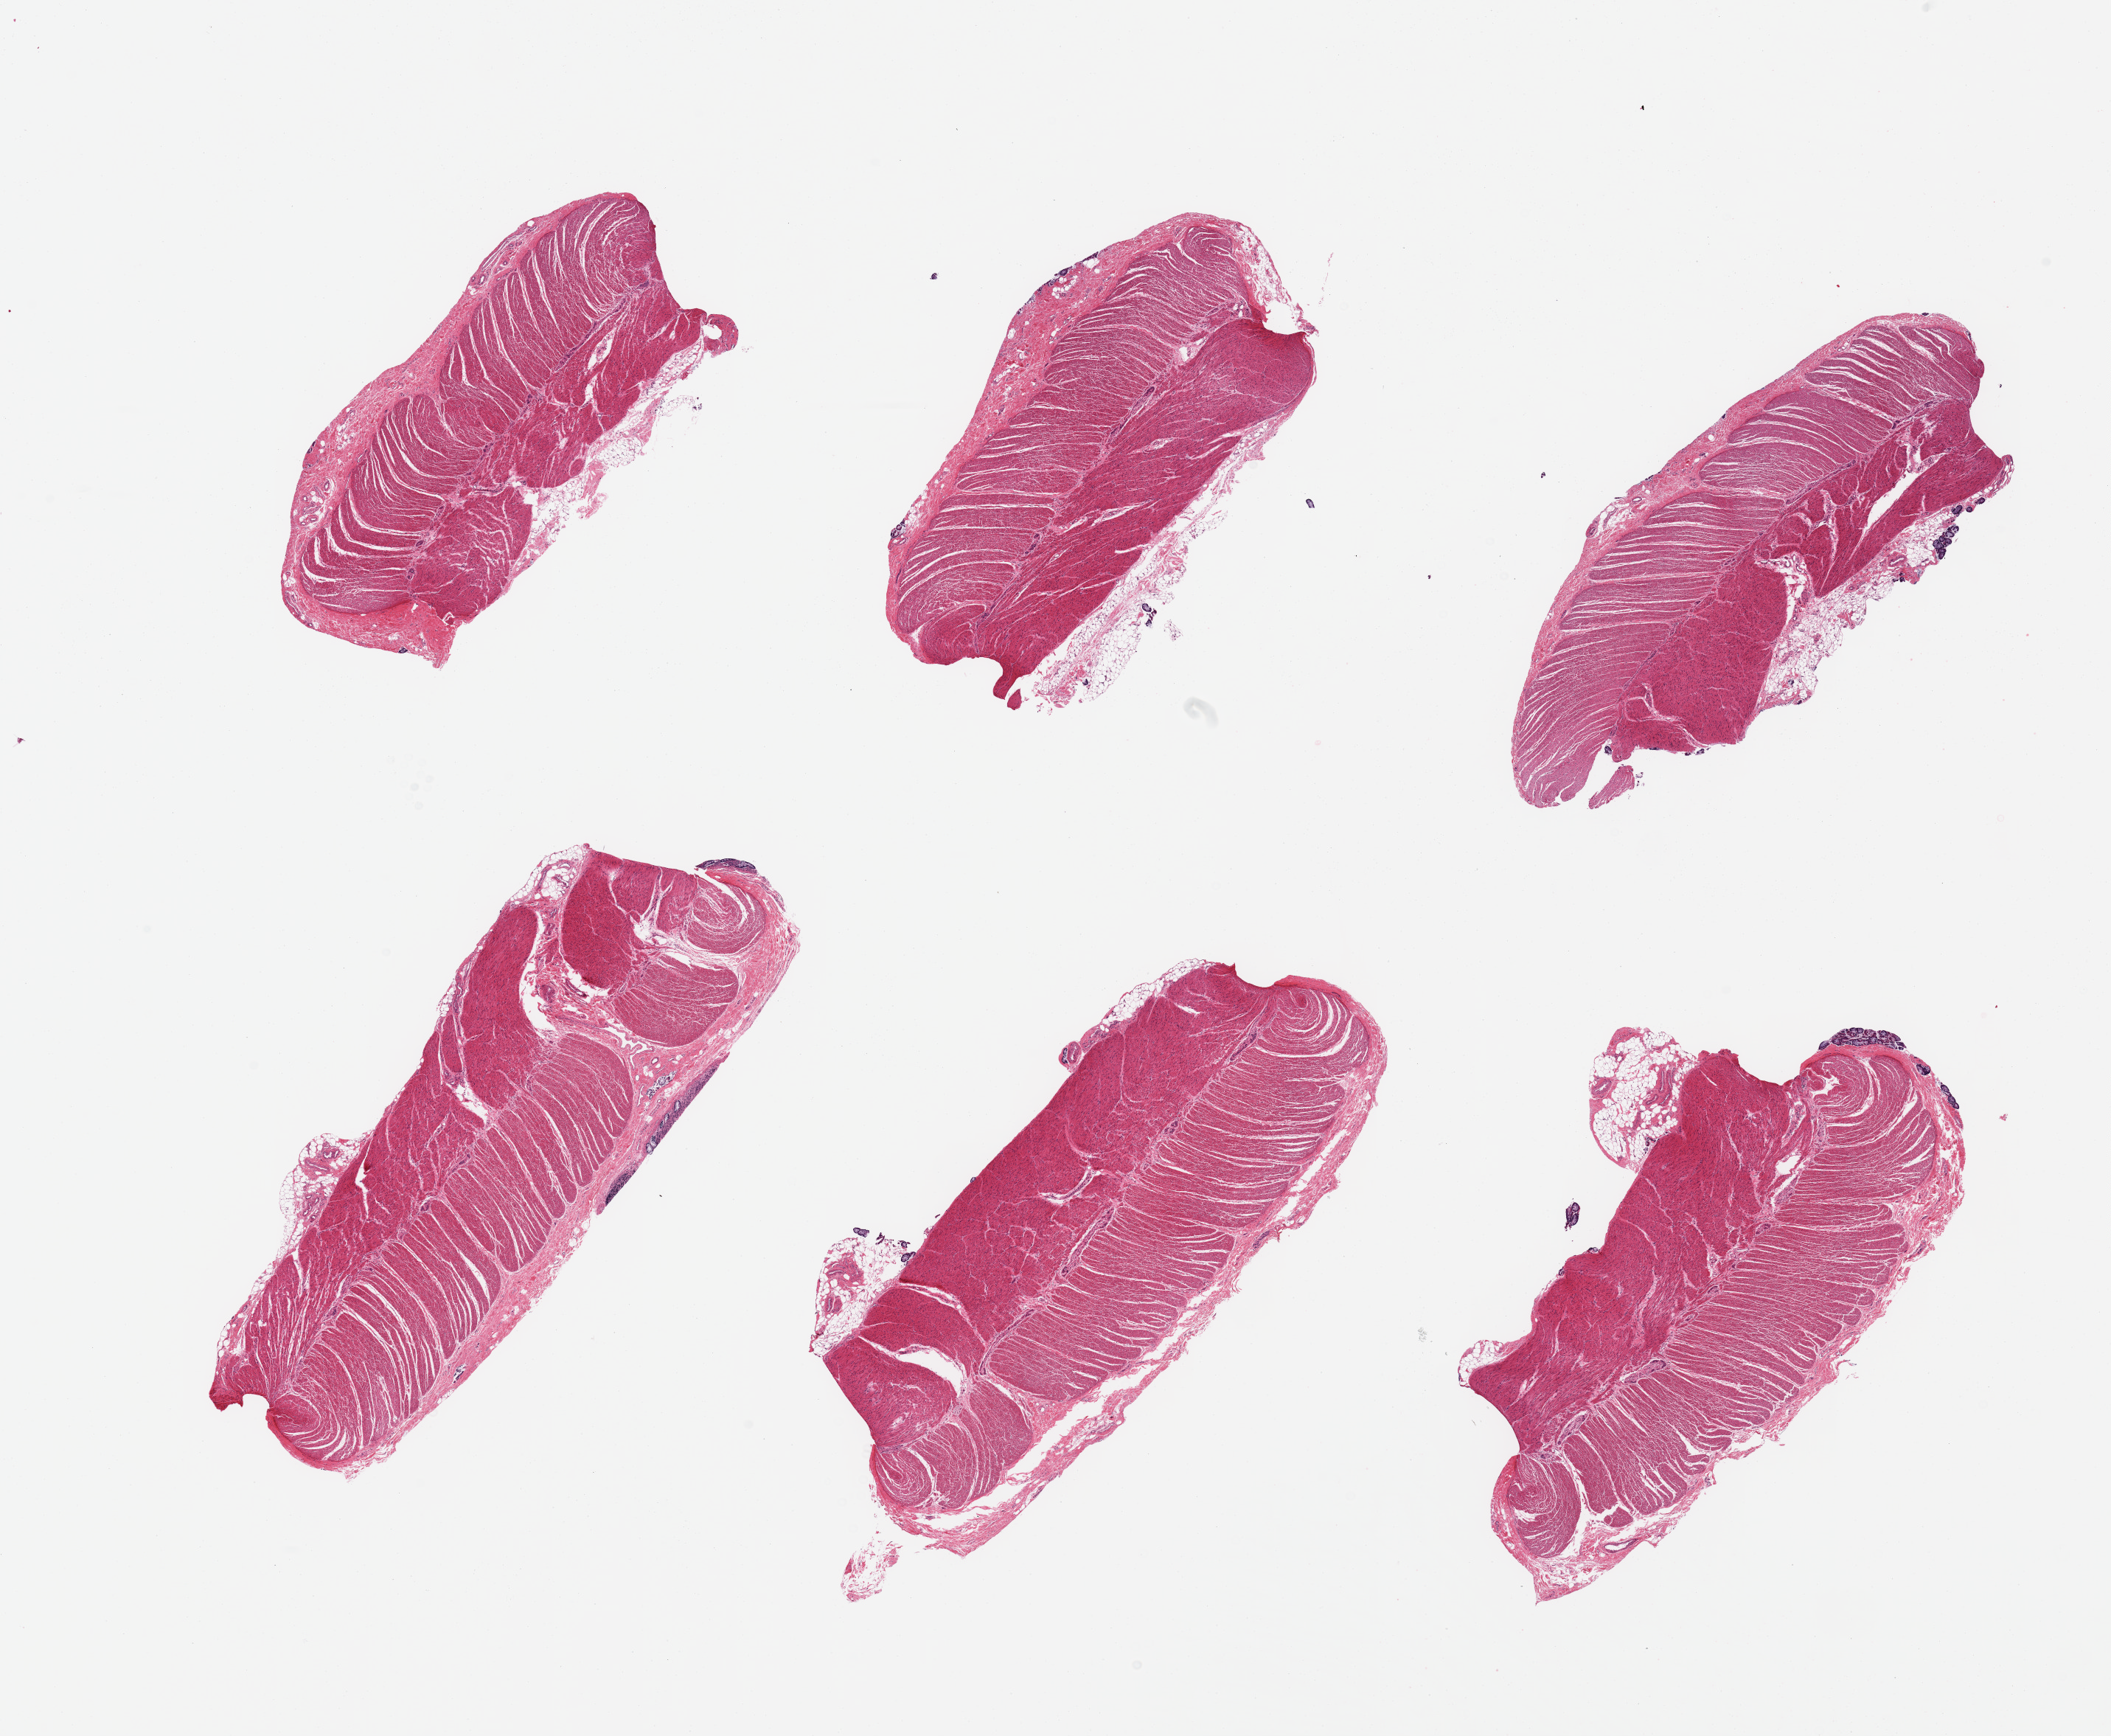
Hematoxylin and eosin (H&E) whole-slide image, brightfield — a low-resolution overview of the entire scanned area, about 22.6 x 18.6 mm (slide scanned at 20x); PAXgene-fixed, paraffin-embedded tissue; target tissue: sigmoid colon; donor tissue sample. Donor: male.
Pathologist's review note for this sample: 6 pieces, confirmed target muscularis.